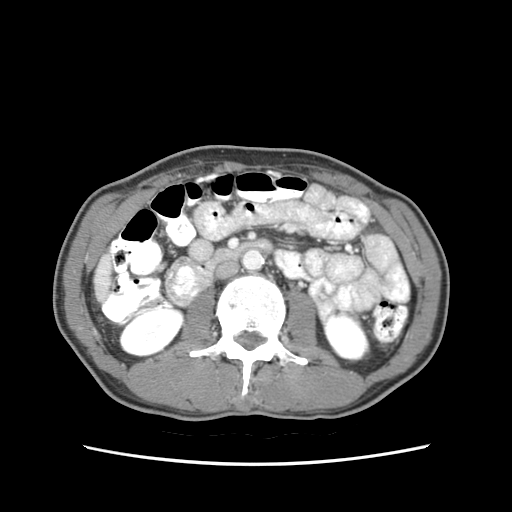
Contrast-enhanced abdominal CT (liver protocol), one axial slice. Slice 9 of 79 in the series (ordered by position). Reconstruction kernel STANDARD. Soft-tissue window (W 400 / L 40 HU). 2.5 mm slice thickness. 512 × 512 image matrix. Case-level facts recorded for this patient, not image findings: diagnosis: hepatocellular carcinoma (patient treated with transarterial chemoembolisation; whether this scan precedes or follows treatment is not stated here); TNM stage (as recorded): Stage-IIIB; Child-Pugh class: A.
Annotated regions visible in this slice (semi-automatic segmentation, software-assisted and operator-edited):
- liver parenchyma outside the tumour (the mass and vessels are separate outlines, so this box may not span the whole liver): bounding box (x1, y1, x2, y2) in pixels: (96, 254, 114, 297)
- liver vessels: (110, 261, 114, 266)